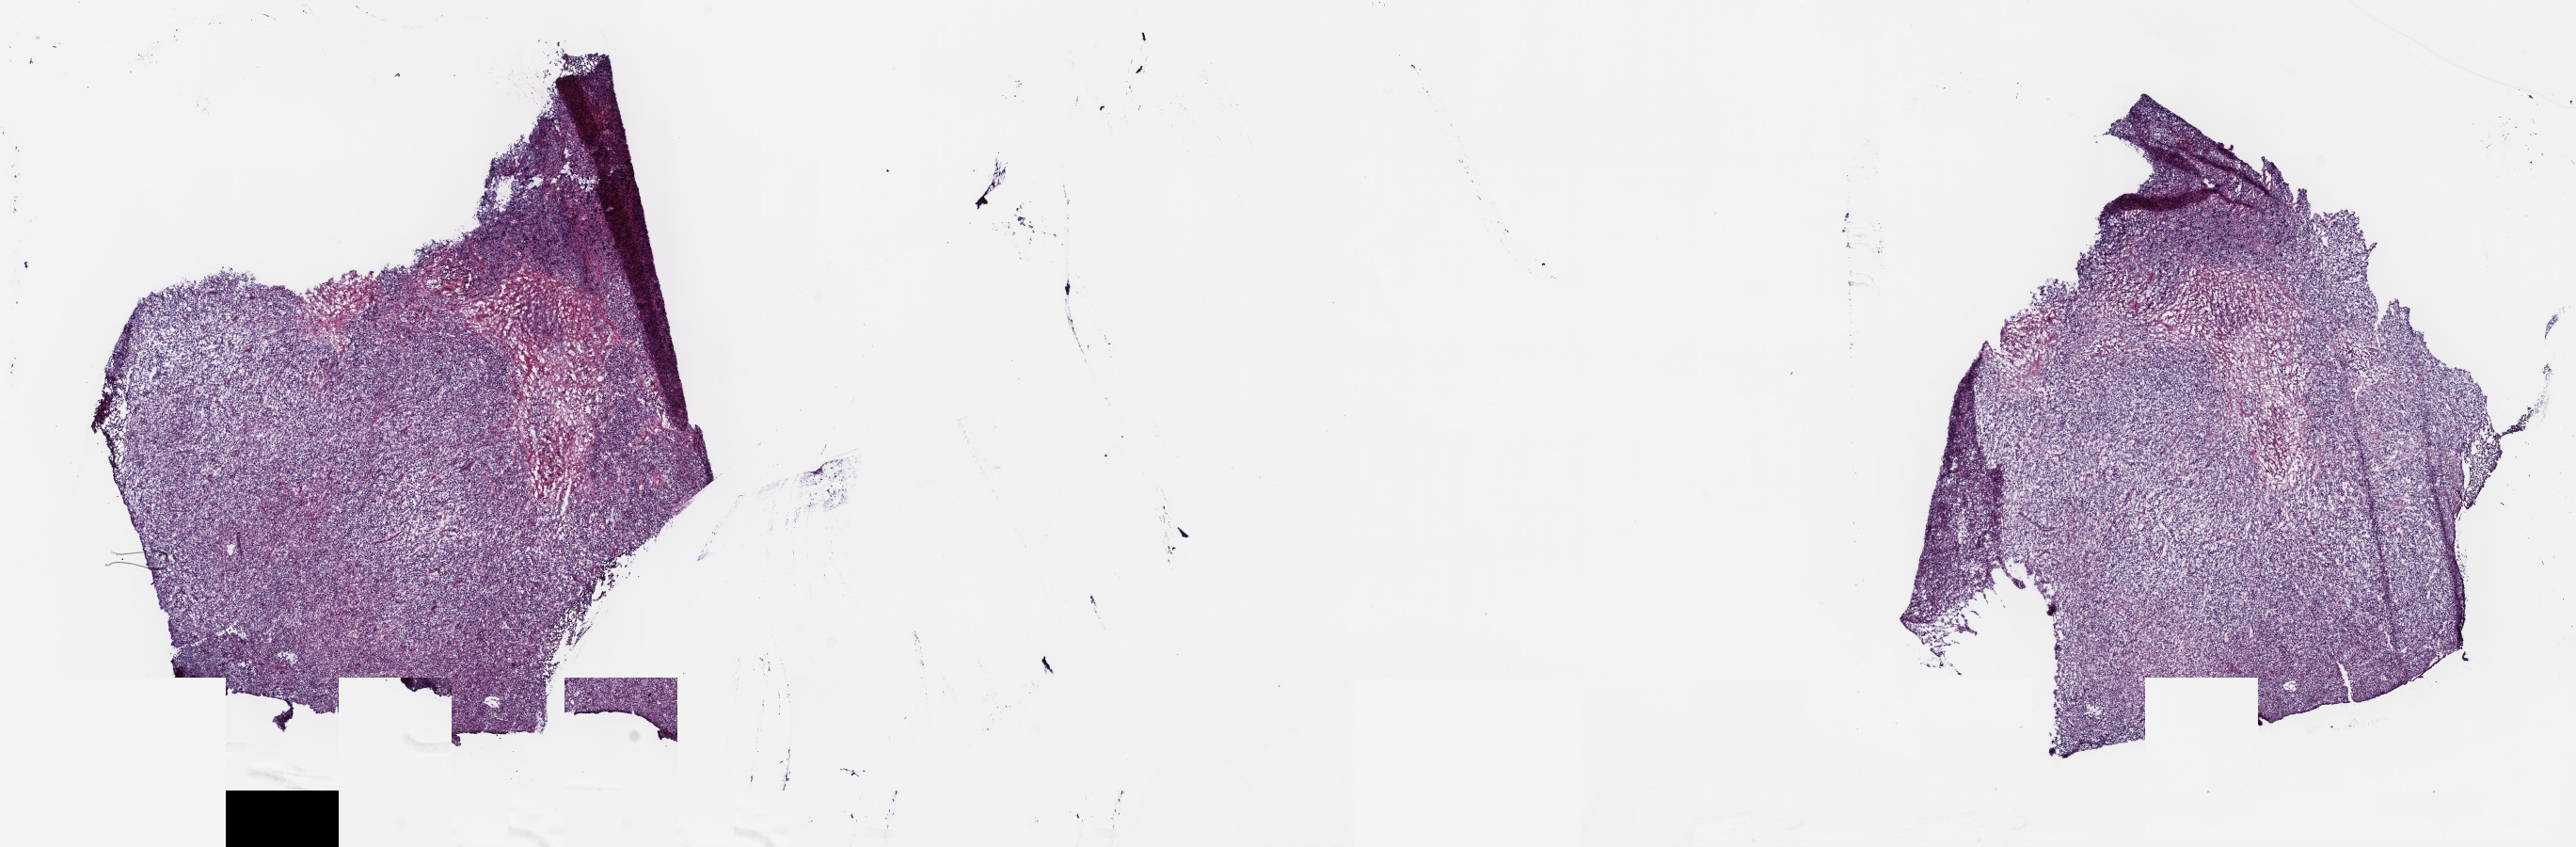
H&E-stained whole-slide image, a low-resolution overview of the entire scanned area, about 22.1 x 7.3 mm; frozen section from the top of the tissue portion; lymphoid tissue, primary tumour sample. Female patient; age at initial diagnosis 23 years. Composition of this section per pathologist review: tumour cells 85%, tumour nuclei 90%, normal cells 0%, stromal cells 15%, necrosis 0%. Inflammatory infiltration, as recorded: lymphocyte infiltration 85%, monocyte infiltration 5%, neutrophil infiltration 5%.
* pathologic diagnosis: Mediastinal (thymic) large B-cell lymphoma (lymph nodes of axilla or arm)